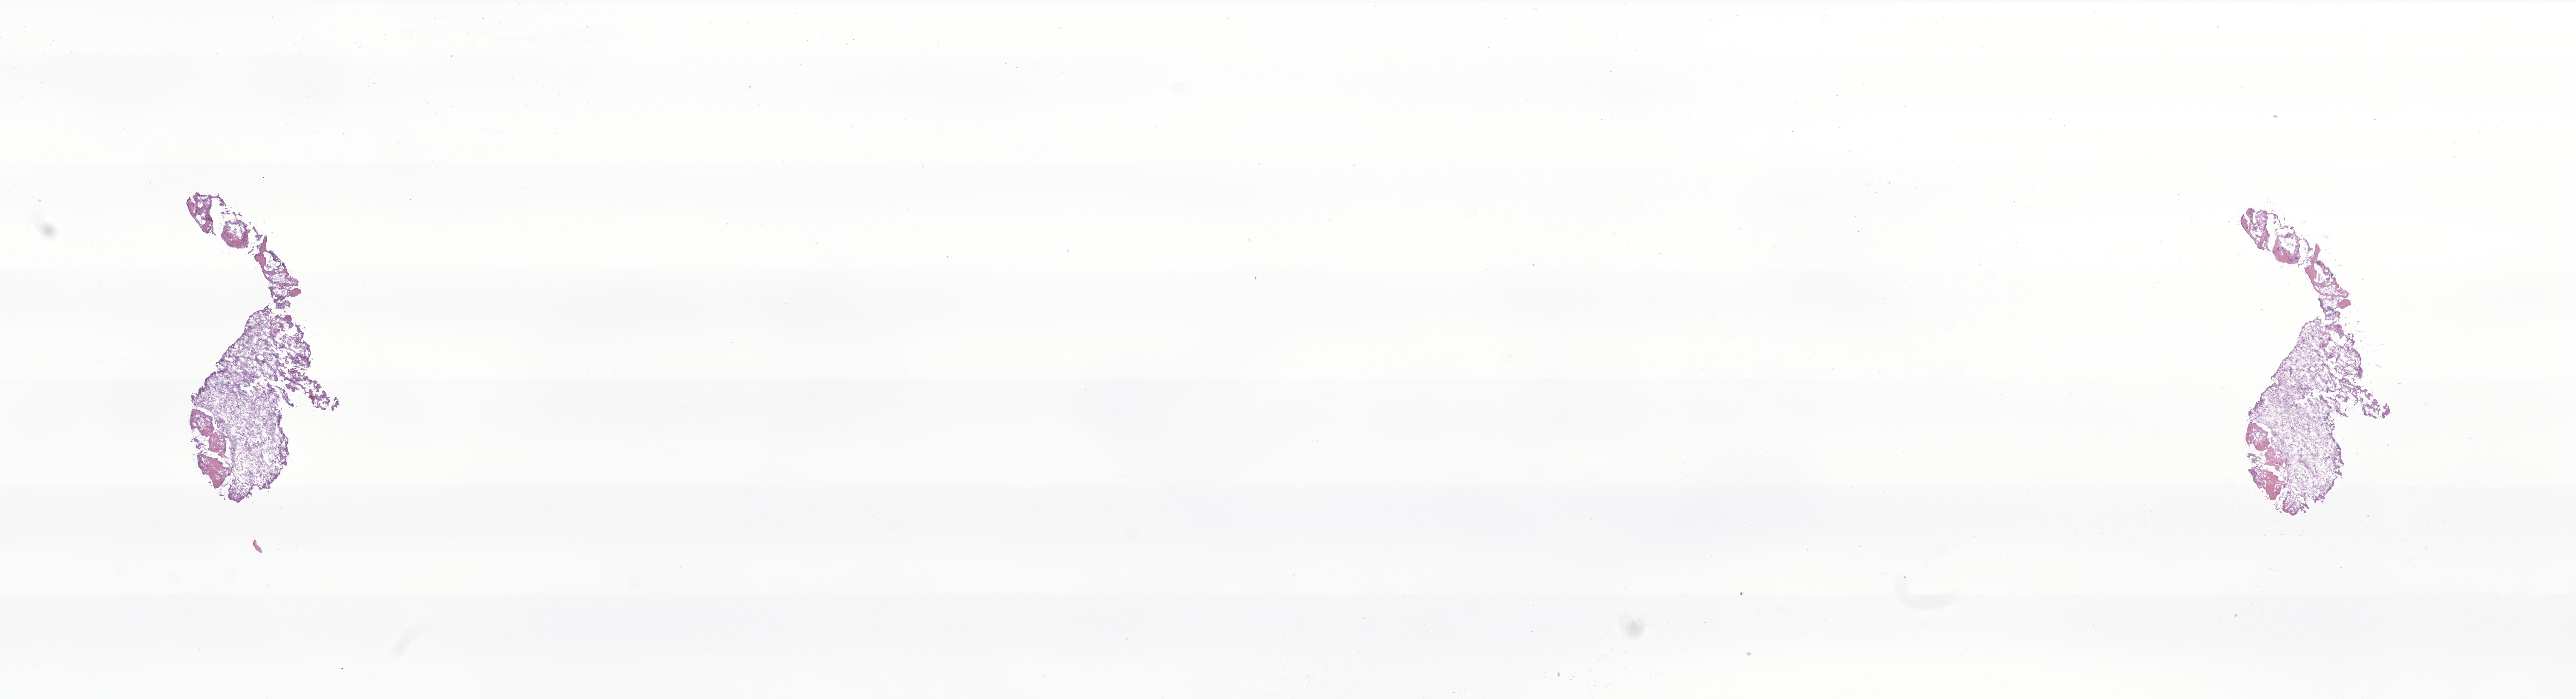
Digitized haematoxylin and eosin-stained section of tumor tissue from the brain — a low-resolution overview of the entire scanned area, about 25.5 x 6.9 mm, frozen section (OCT-embedded). Female patient, age 131 months (10 years 11 months).
- diagnosis (ICD-O-3 morphology term): Neoplasm, uncertain whether benign or malignant